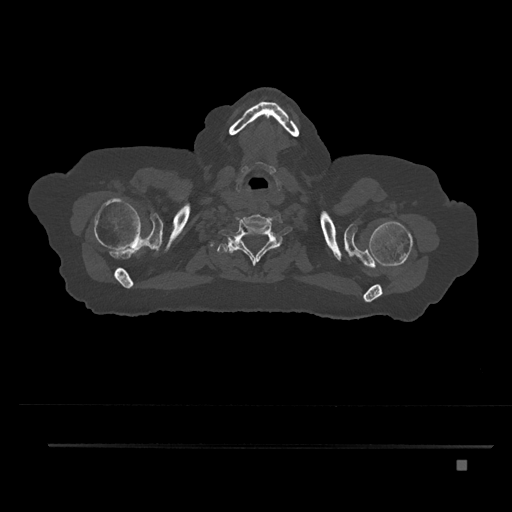
CT including the spine, one axial slice. Reconstruction kernel Br40s/3. 120 kVp. Bone window (W 1800 / L 400 HU). 0.5 mm slice thickness. 512 × 512 image matrix. Female patient, age 76 years. Case-level facts recorded for this patient, not image findings: primary cancer: lung.
Structures marked on this image (semi-automatic segmentation, software-assisted and operator-edited):
- T1 vertebra: bounding box <222,240,265,256> (left, top, right, bottom; pixels)